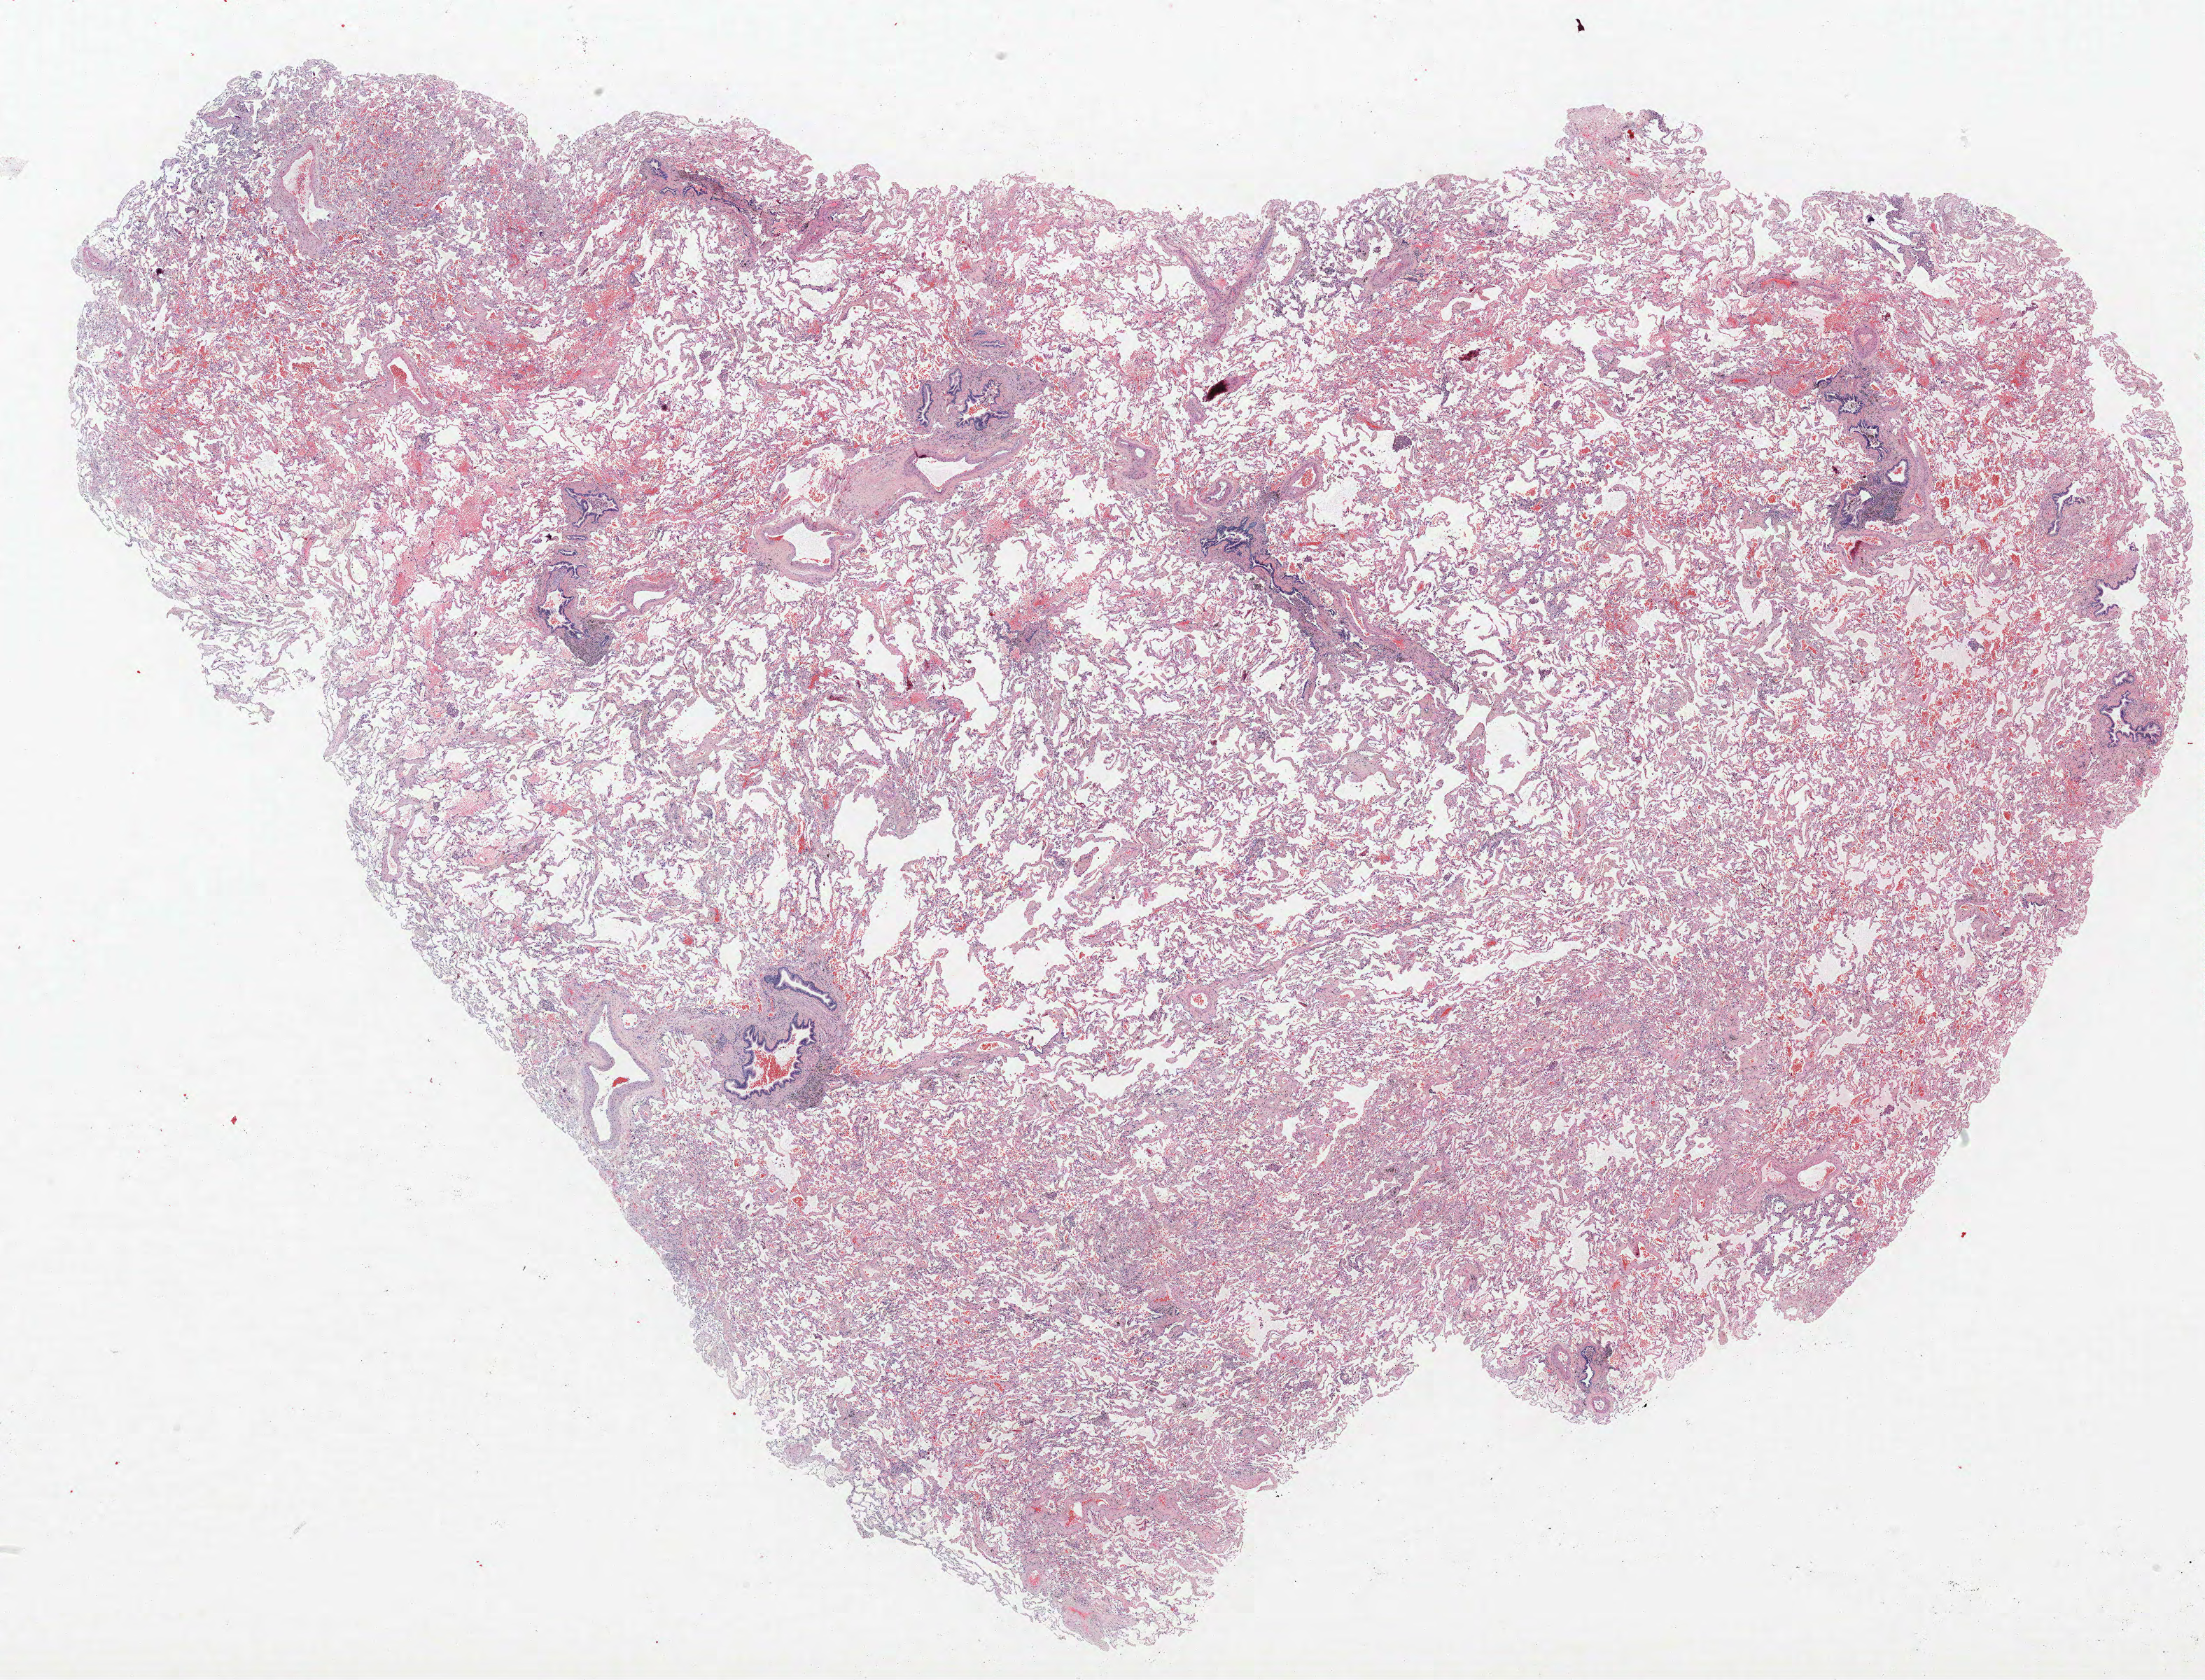
Hematoxylin and eosin (H&E) stained whole-slide image, a low-resolution overview of the entire scanned area, about 25.2 x 19.2 mm (slide scanned at 40x). FFPE section. Lung tissue. Female patient, aged 64 at enrolment. Grade: well differentiated (G1).
Stage (AJCC 6th edition): IA. Primary tumour location (clinical record): right upper lobe. Participant's lung-cancer diagnosis: Bronchiolo-alveolar adenocarcinoma, NOS (ICD-O-3 8250/3). Tumour size (pathology): 10 mm.